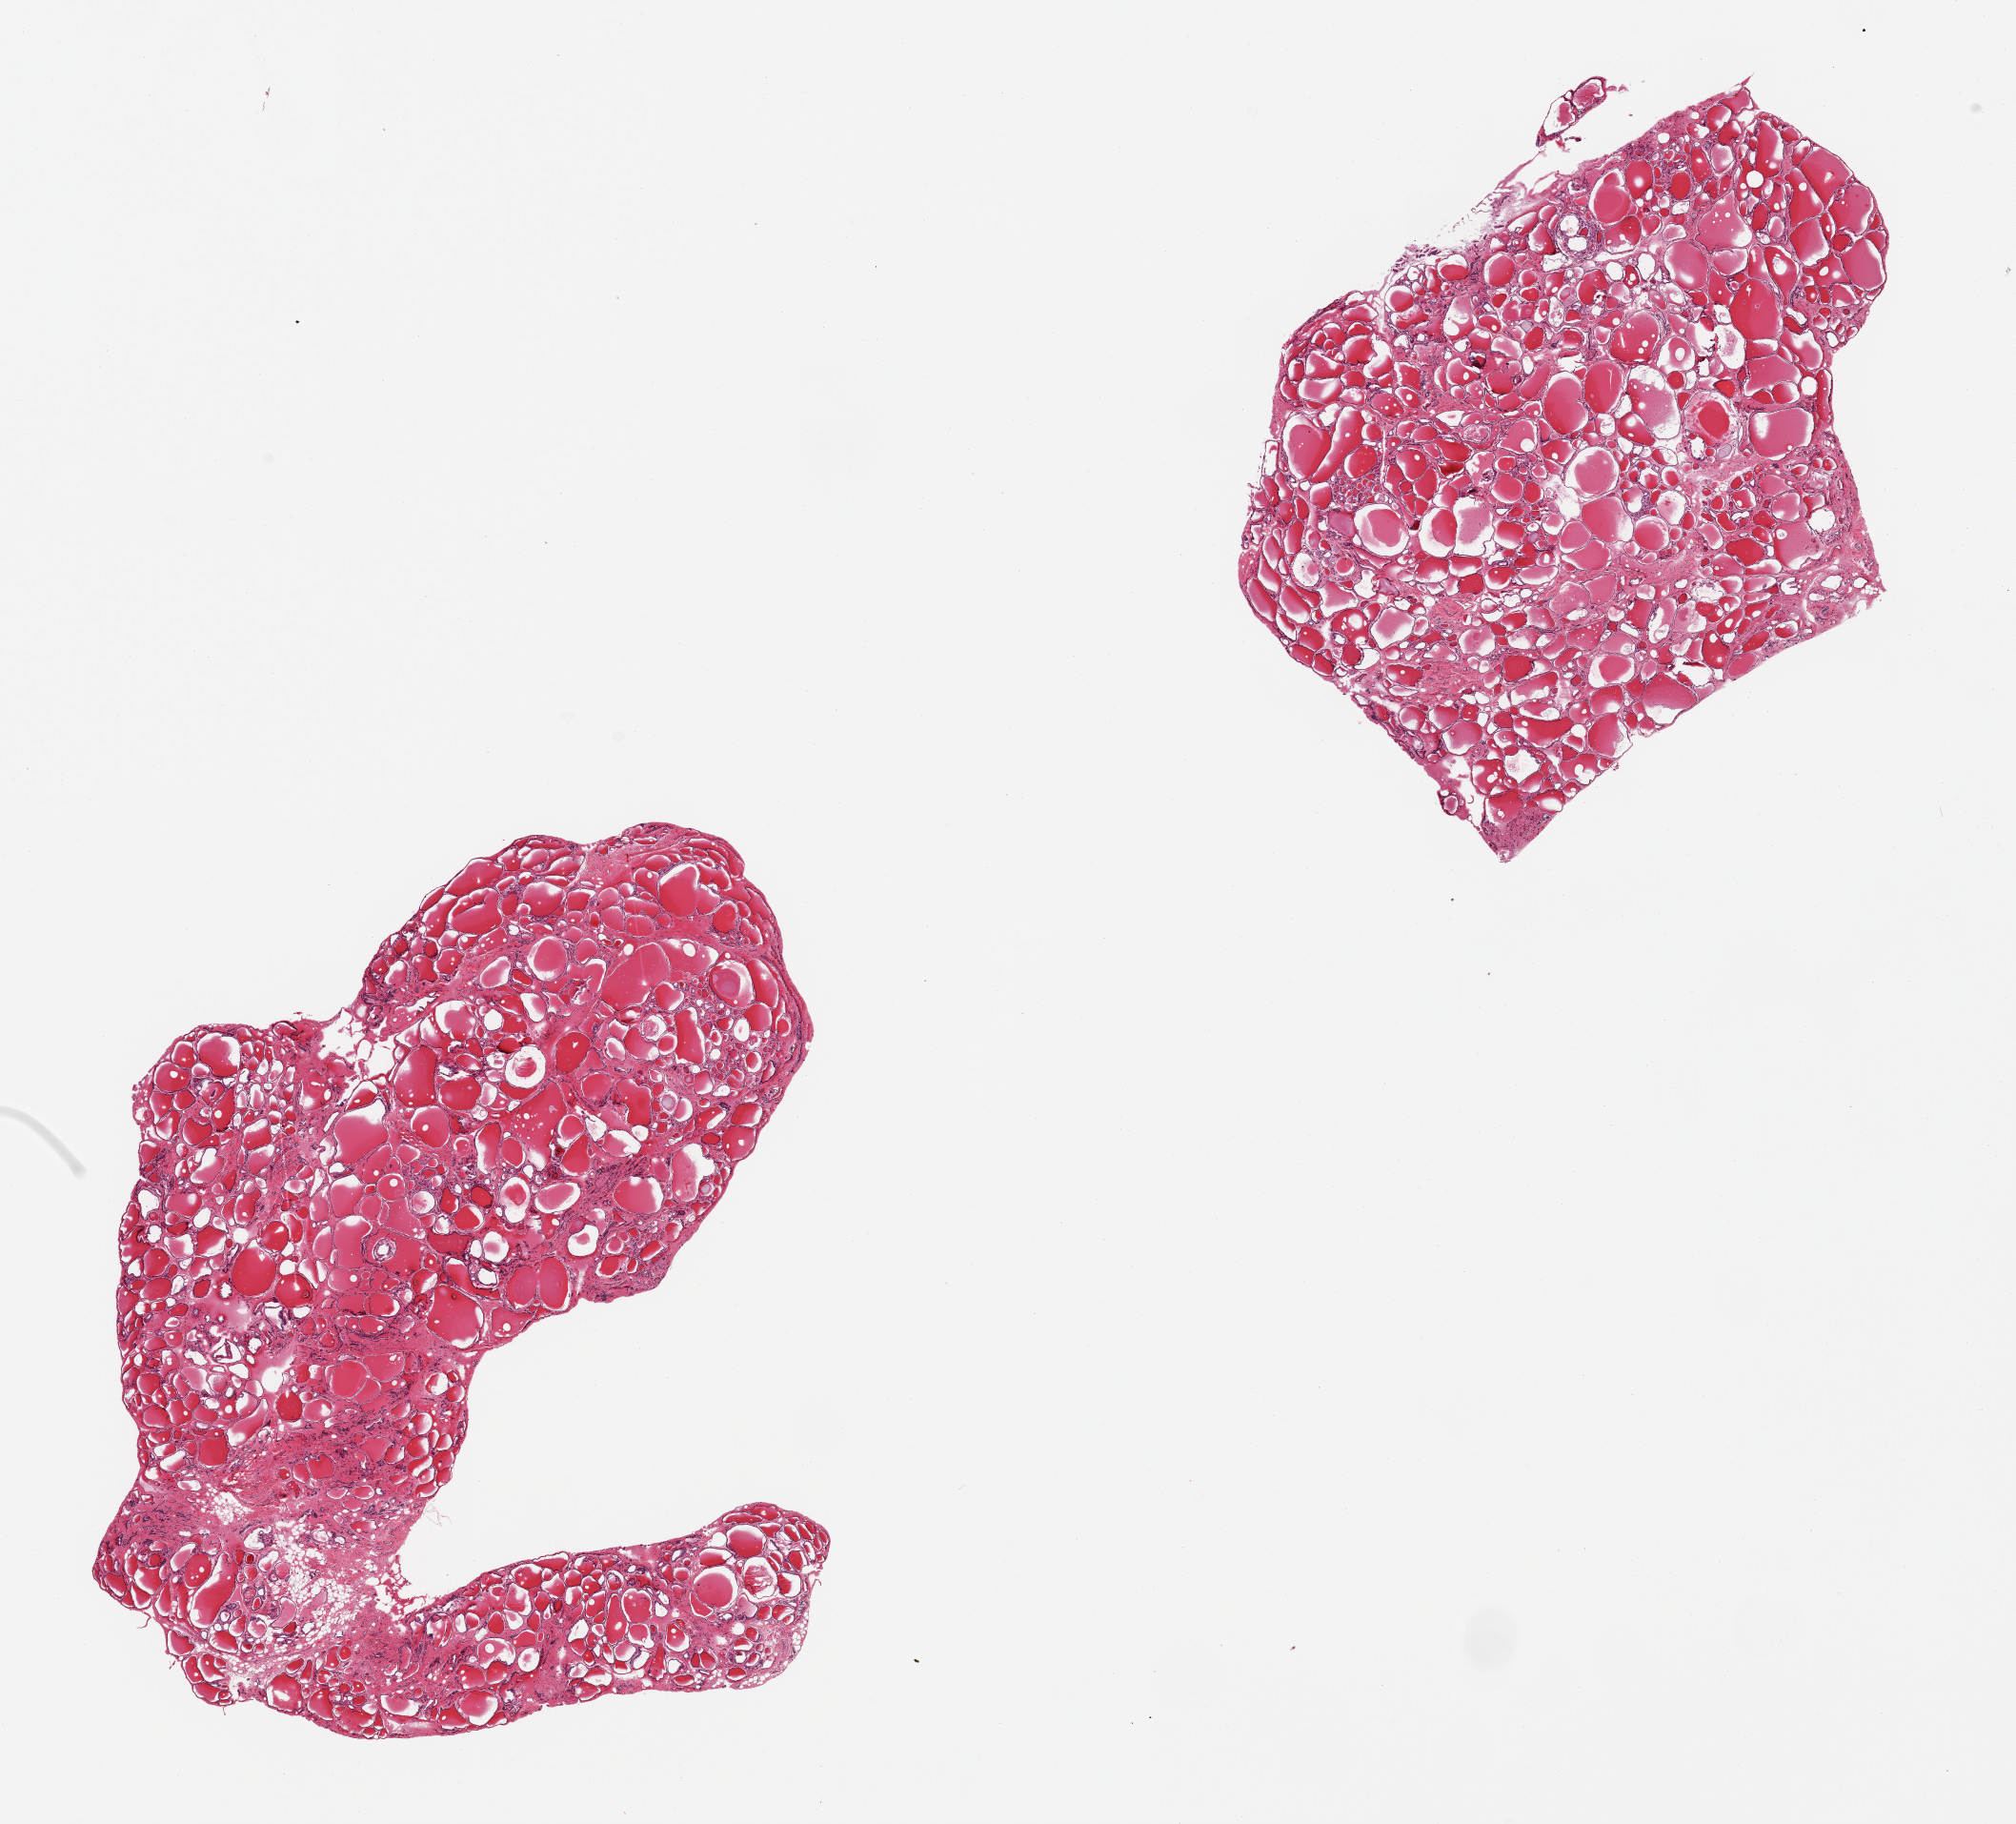
Digitized H&E-stained section, whole scanned area (about 16.7 x 15.1 mm) shown as a low-resolution overview; PAXgene-fixed, paraffin-embedded tissue; target tissue: thyroid; tissue donor sample. Donor: male.
- pathologist's review note for this sample: 2 pieces; variably sized follicles, some fibrosis